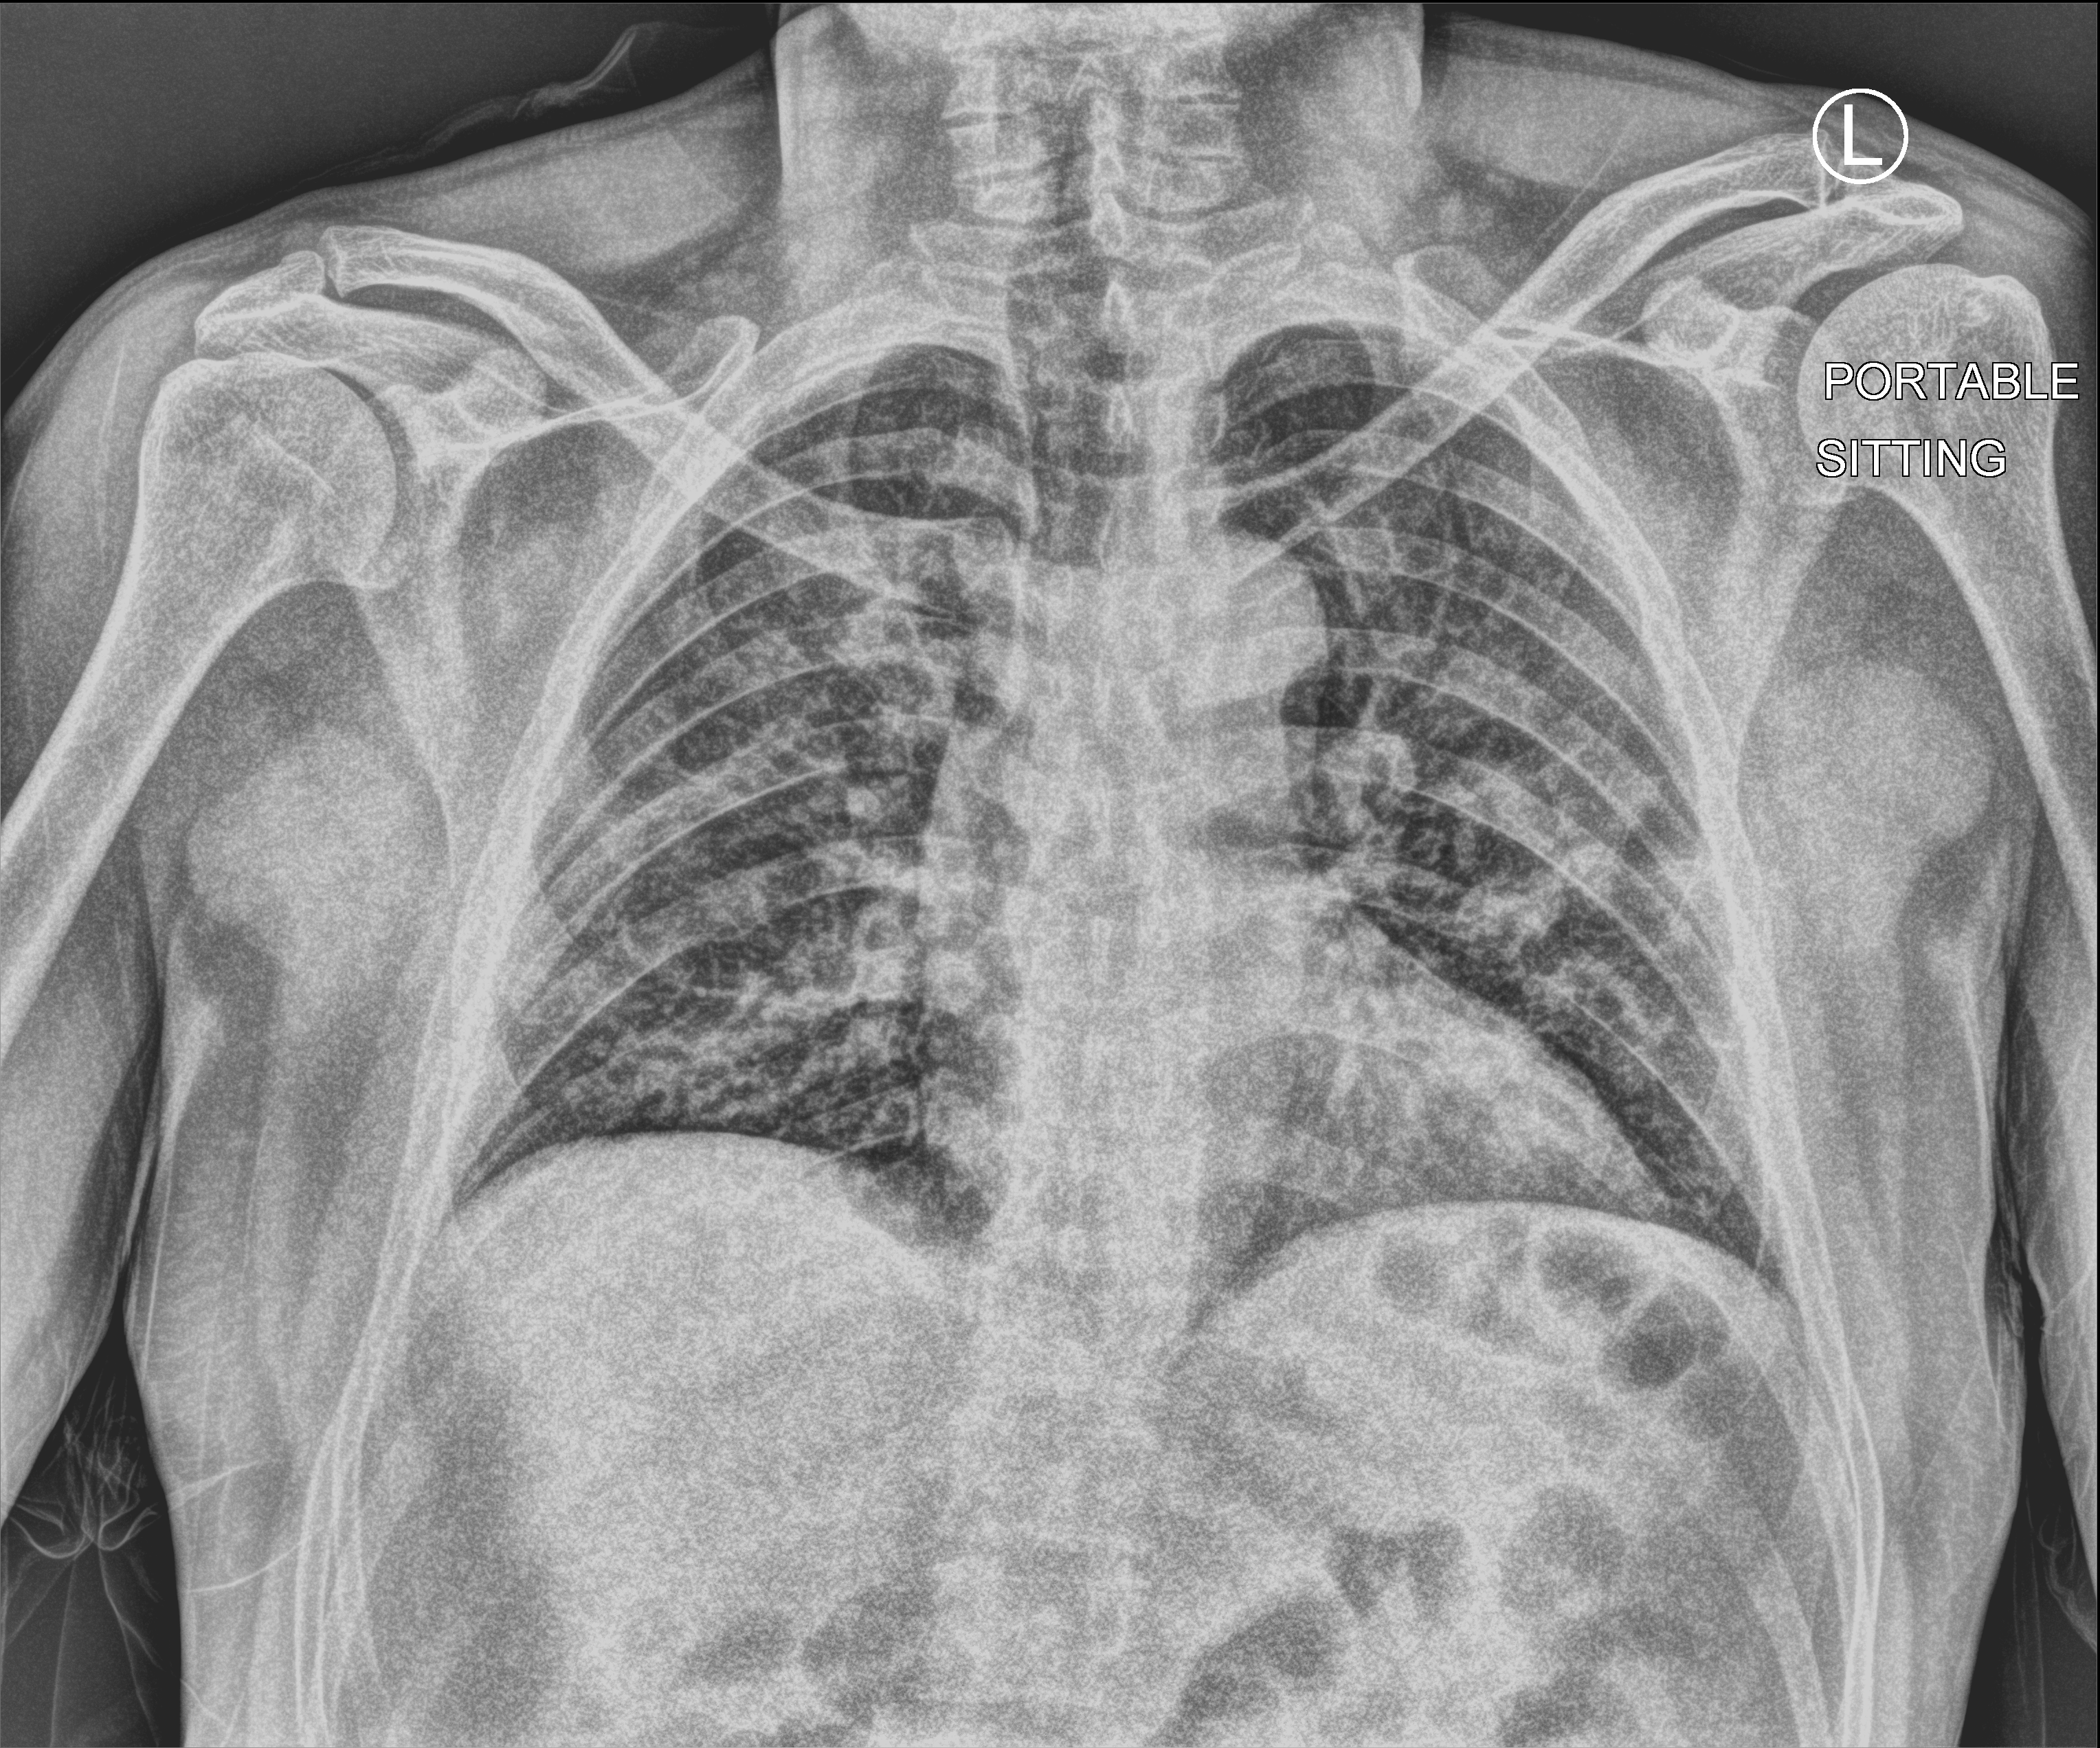
Chest X-ray (portable); anteroposterior (AP) projection. Patient hospitalised with COVID-19; male, aged 18–59 years.
Admission-level facts for this patient (not findings on this image; timing relative to this image not recorded): admitted to intensive care during this hospital stay: no; chronic kidney disease (admission record): no.